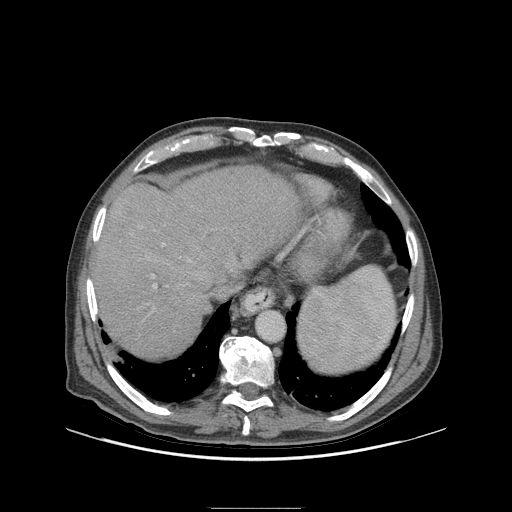
Contrast-enhanced abdominal CT (liver protocol), one axial slice. 140 kVp. Soft-tissue window (W 400 / L 40 HU). 512 × 512 image matrix. Case-level facts recorded for this patient, not image findings: diagnosis: hepatocellular carcinoma (patient treated with transarterial chemoembolisation; whether this scan precedes or follows treatment is not stated here); TNM stage (as recorded): Stage-I.
Structures marked on this image (semi-automatically segmented with operator editing):
- abdominal aorta: bounding box [x1, y1, x2, y2] px = [256, 311, 284, 340]
- liver parenchyma outside the tumour (the mass and vessels are separate outlines, so this box may not span the whole liver): [92, 166, 300, 356]
- liver vessels: [153, 244, 191, 289]